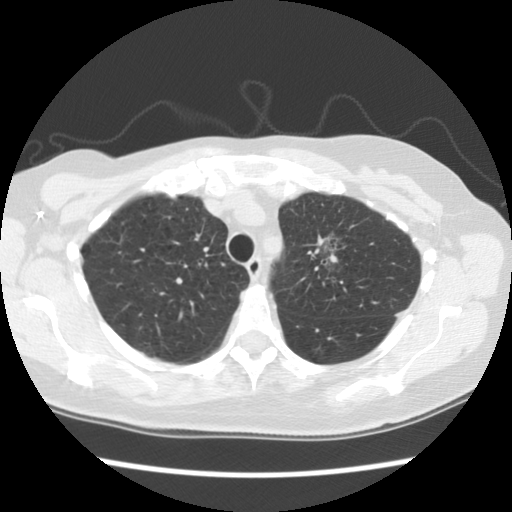
Axial slice from a low-dose chest CT screening exam. Second annual screen. Lung window (W 1500 / L -600 HU). Standard (soft-tissue) reconstruction kernel (STANDARD). Slice 82 of 110 in the series. Female participant, aged 65 years at enrolment. Former smoker at enrolment.
- Lesion marked by an expert reader, bounding box <301,223,363,284> (left, top, right, bottom; pixels).
- The screening reader recorded 2 non-calcified nodules or masses ≥4 mm on this exam (right upper lobe, left upper lobe); which of them this box marks is not recorded.
- Later outcome: lung cancer diagnosed 481 days after this screen (after the third annual screen) — adenocarcinoma, NOS, left upper lobe, moderately differentiated (G2), stage IA (AJCC 6th edition), 30 mm at pathology.